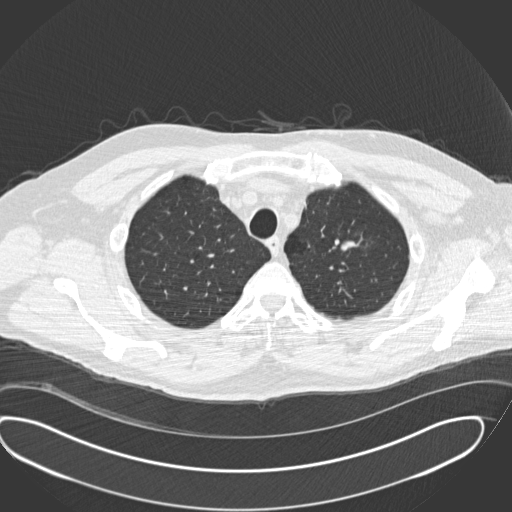
Chest CT (low-dose screening protocol), one axial image. Second screening round (one year after baseline). Lung window (W 1500 / L -600 HU). 120 kVp. Slice 39 of 190 in the series. 512 × 512 image matrix, field of view 418 × 418 mm. Male, age 56 years at enrolment. Current smoker at enrolment.
Expert-annotated lung lesion, bounding box [x1, y1, x2, y2] px = [312, 227, 370, 271]. No non-calcified nodule or mass ≥4 mm was recorded by the screening reader at this exam.